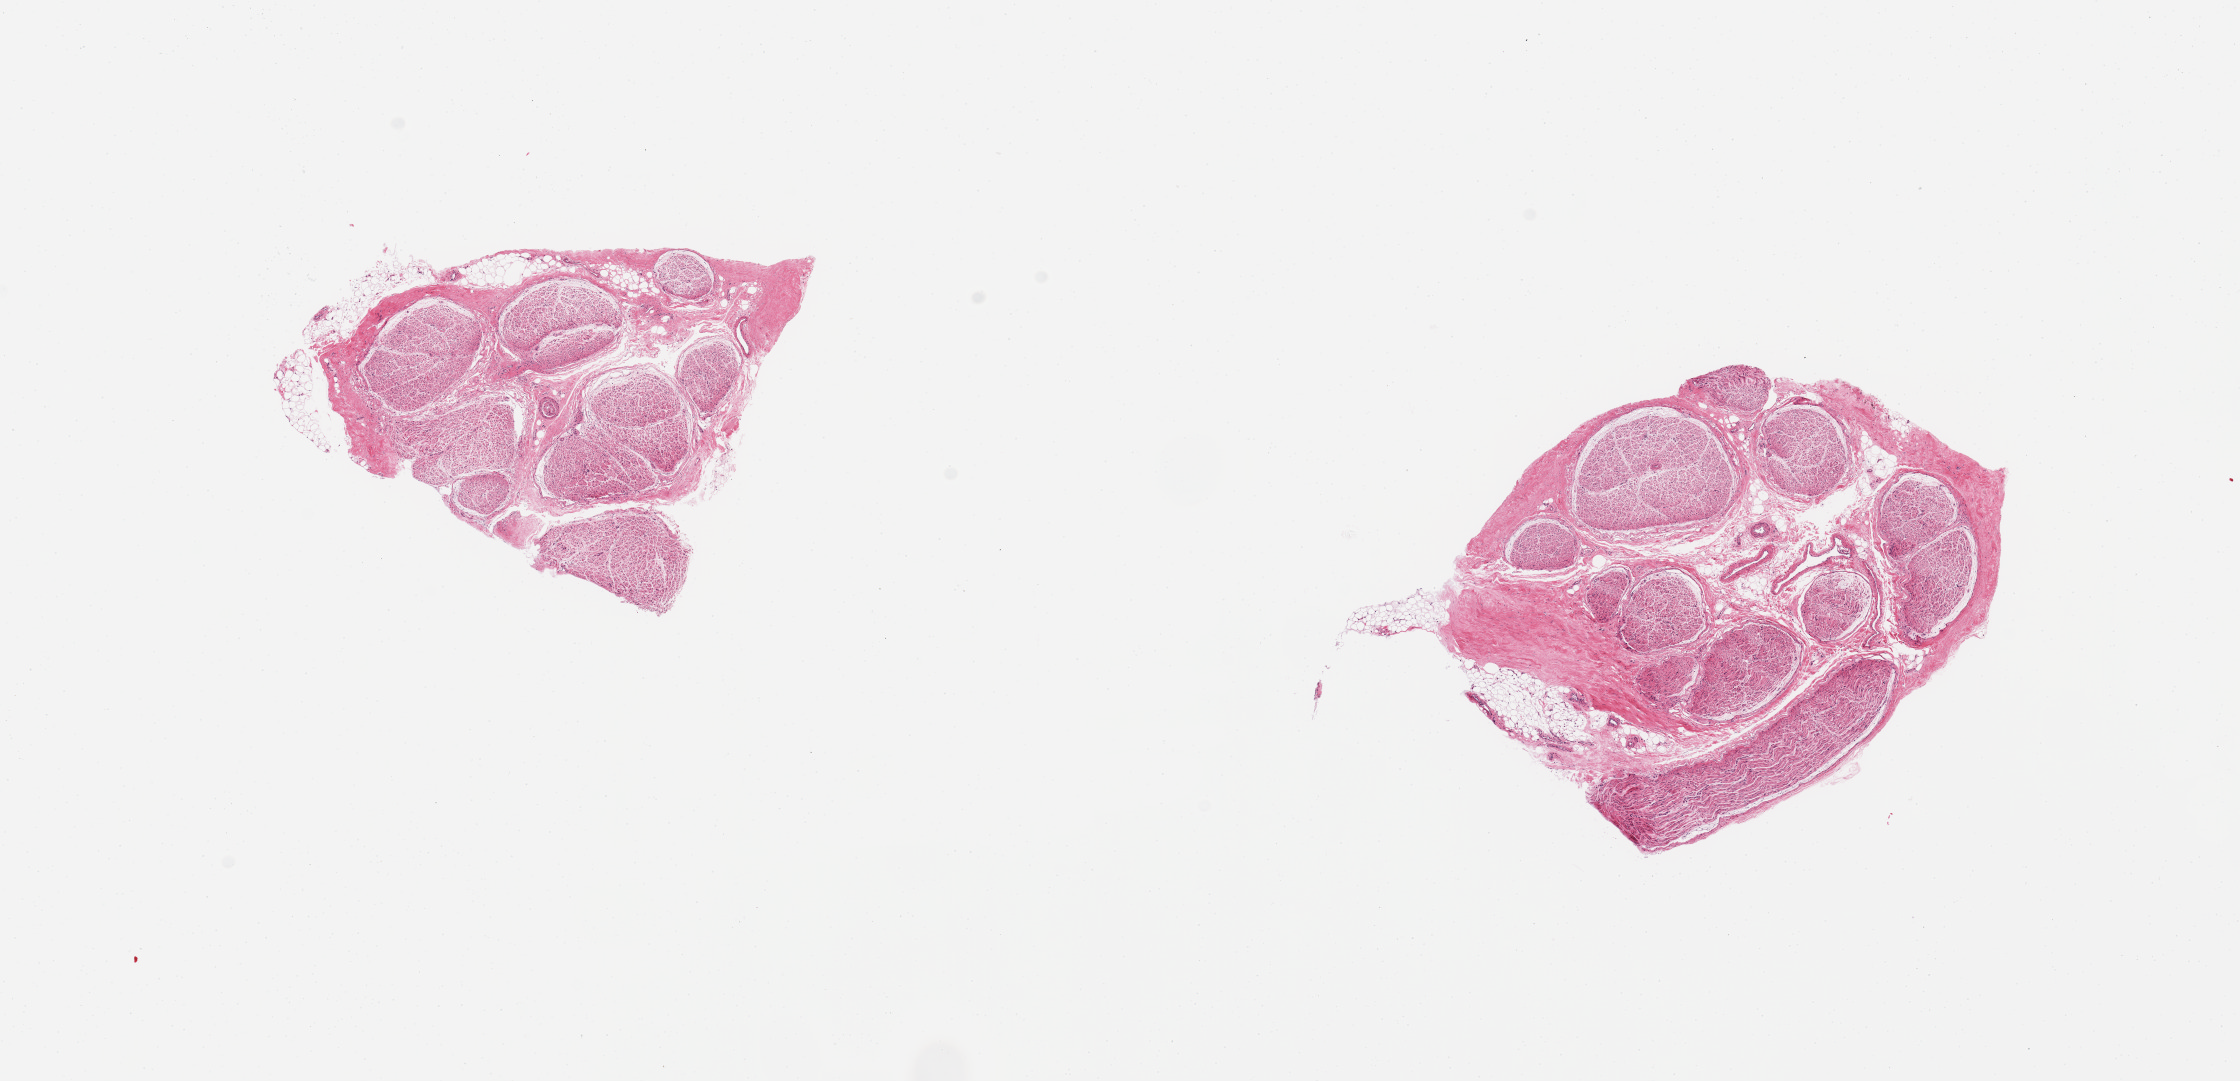
Whole-slide image, hematoxylin and eosin (H&E) stain — low-resolution overview of the scanned area, about 17.7 x 8.6 mm; PAXgene-fixed, paraffin-embedded tissue; sampled site (target tissue): tibial nerve; tissue donor sample. Donor: female.
Pathologist's review note for this sample: 2 pieces; well trimmed.